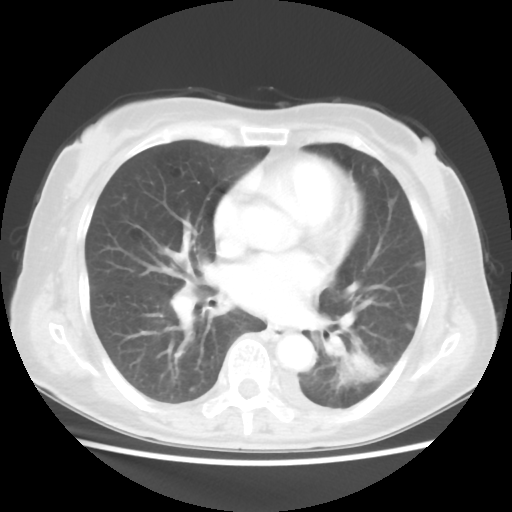
Chest CT, one axial slice. Position 17 of 40 along the scan axis. 100 kVp. Lung window (W 1500 / L -600 HU). 512 × 512 image matrix. Female patient, age 69 years. Case-level facts recorded for this patient, not image findings: clinical TNM (as recorded): T1c N0 M0.
Structures marked on this image (rectangle marked by the reading radiologist):
- lung tumour (recorded histology: adenocarcinoma): bounding box [x1, y1, x2, y2] px = [345, 349, 381, 383]